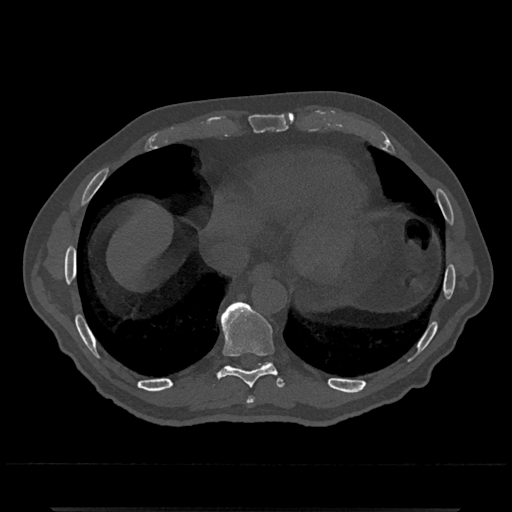
CT including the spine, one axial slice. Position 606 of 797 along the scan axis. Reconstruction kernel Br40s/3. 120 kVp. Bone window (W 1800 / L 400 HU). 512 × 512 image matrix, field of view 393 × 393 mm. Male patient, age 67 years. From the clinical record (not read from this slice): primary cancer: prostate.
Annotated regions visible in this slice (semi-automatic segmentation, software-assisted and operator-edited):
- T10 vertebra: bounding box (x1, y1, x2, y2) in pixels: (264, 363, 267, 365)
- T8 vertebra: (247, 397, 255, 403)
- T9 vertebra: (218, 301, 283, 388)